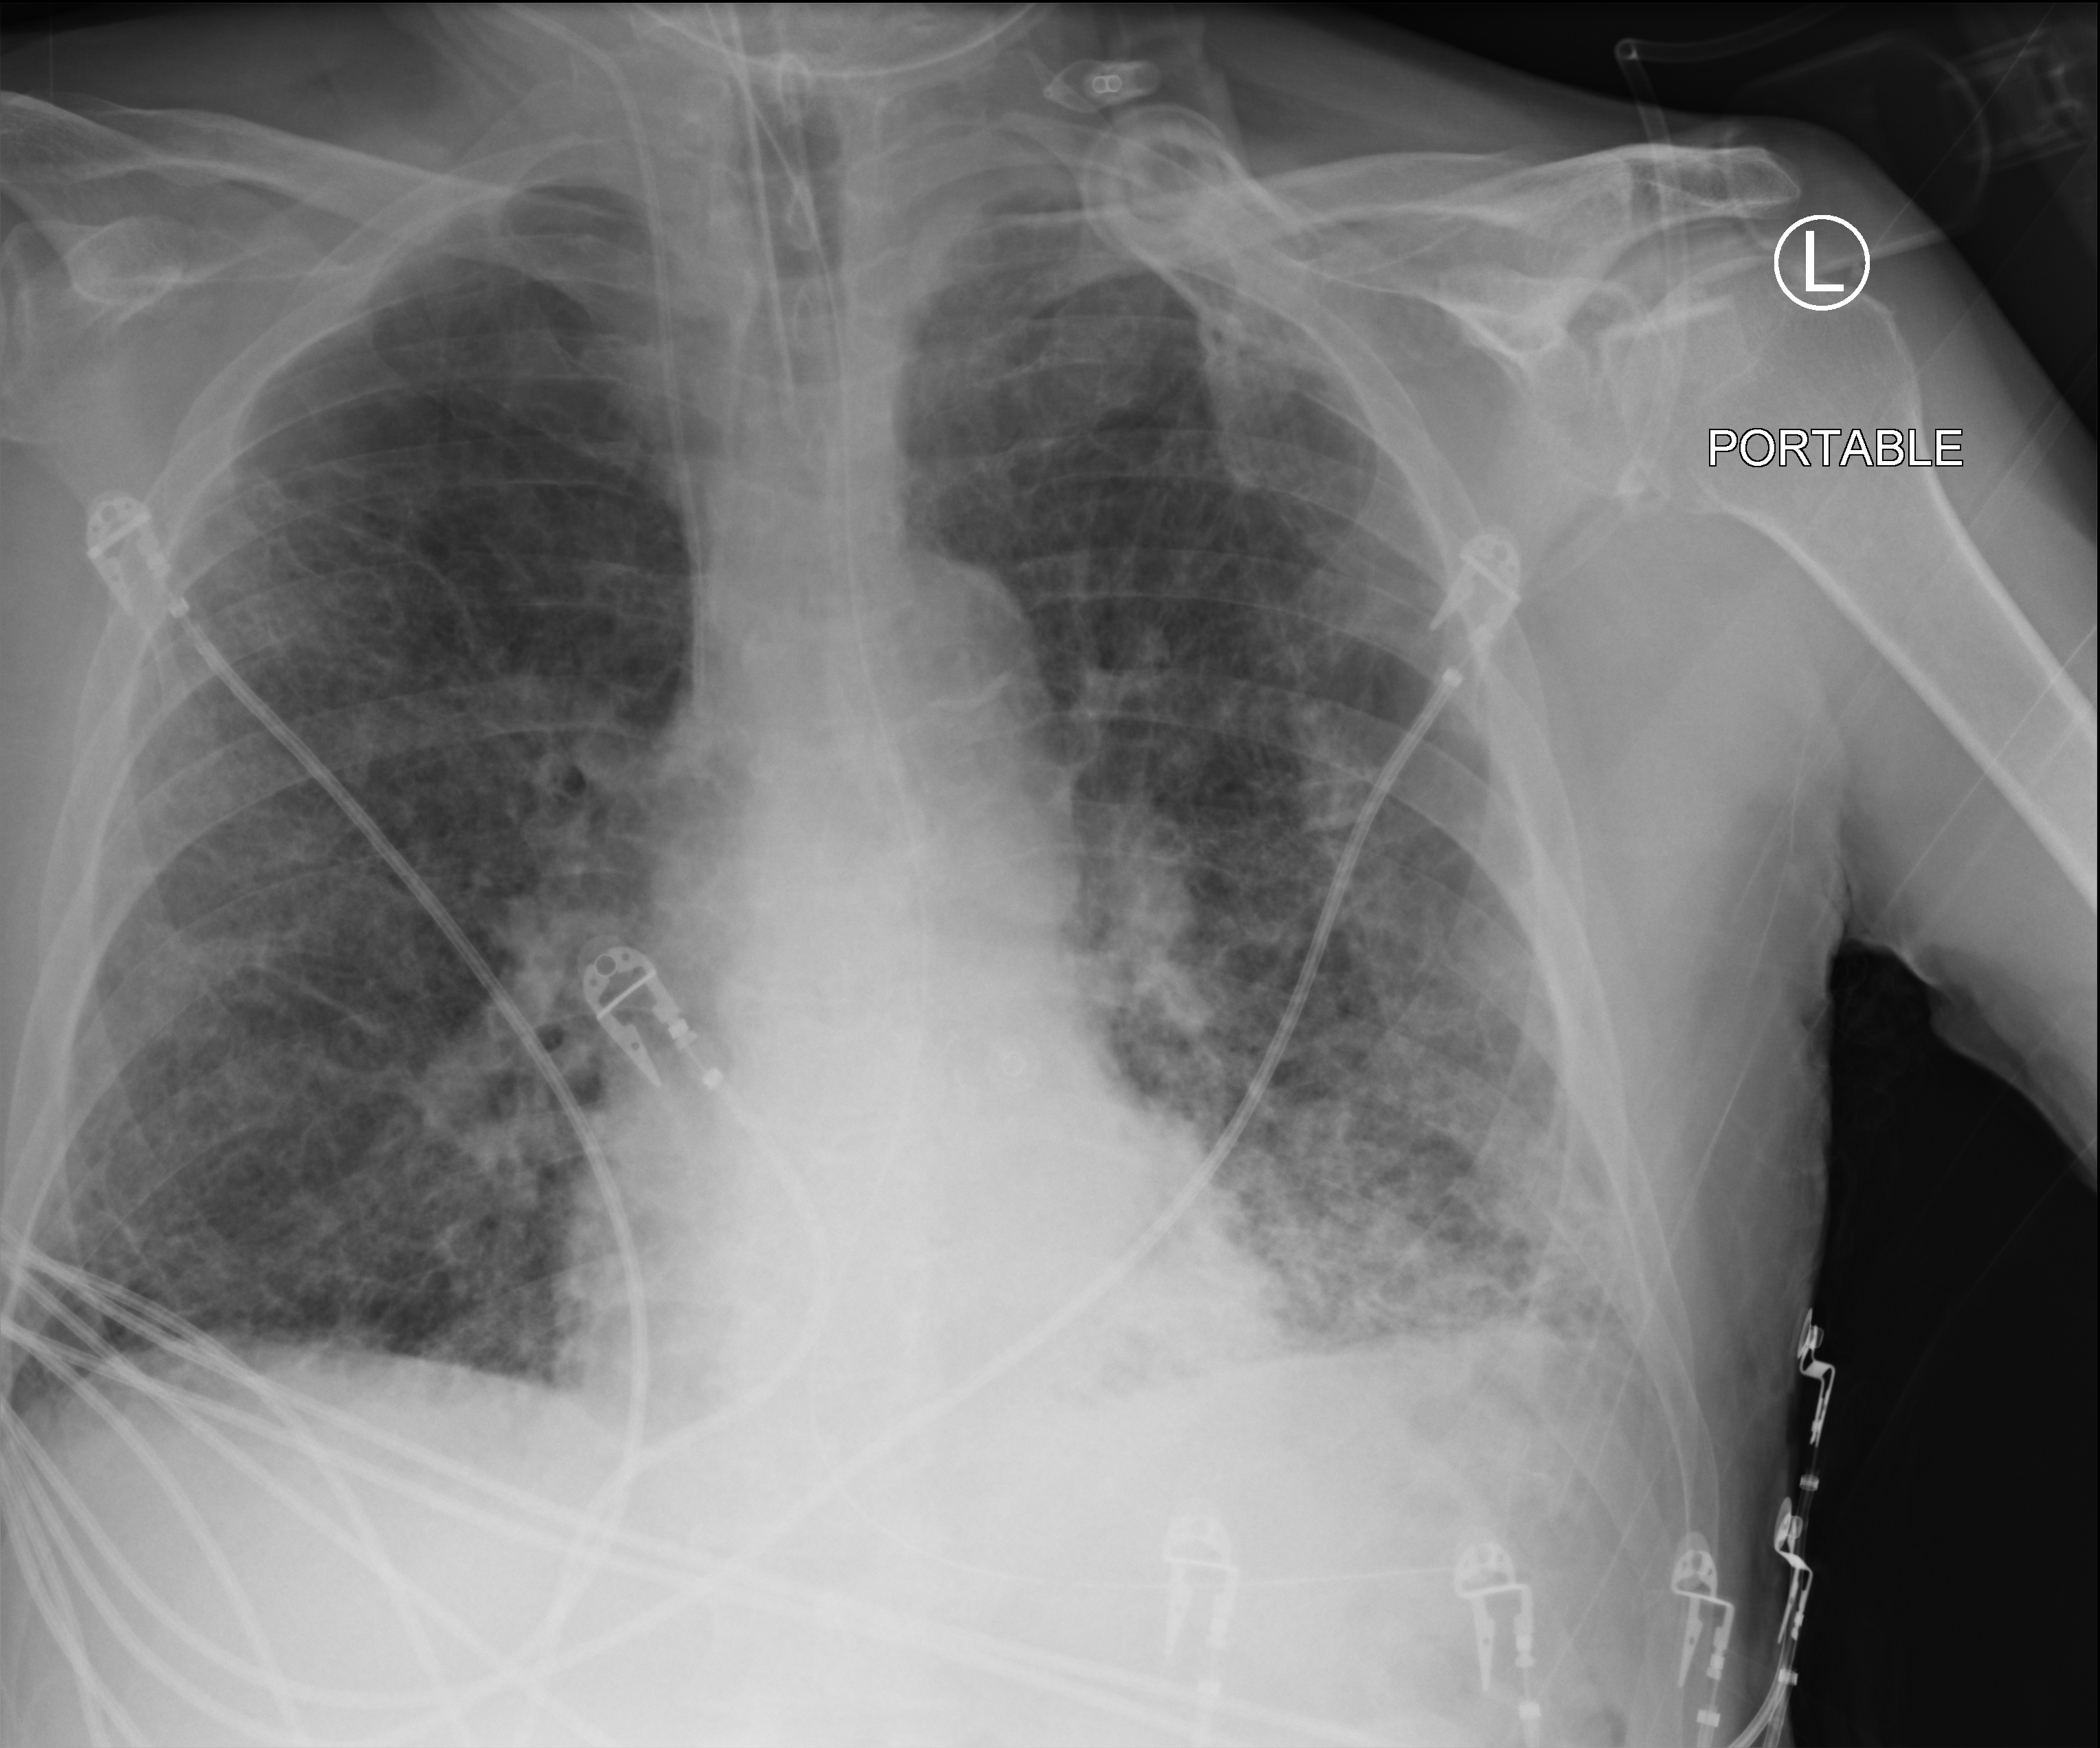
Chest X-ray (portable). Patient hospitalised with COVID-19; male, aged 75–90 years.
Hospital-stay facts (about this admission, not read from this image; timing relative to this image not recorded): diabetes (admission record): no; admitted to intensive care during this hospital stay: yes.